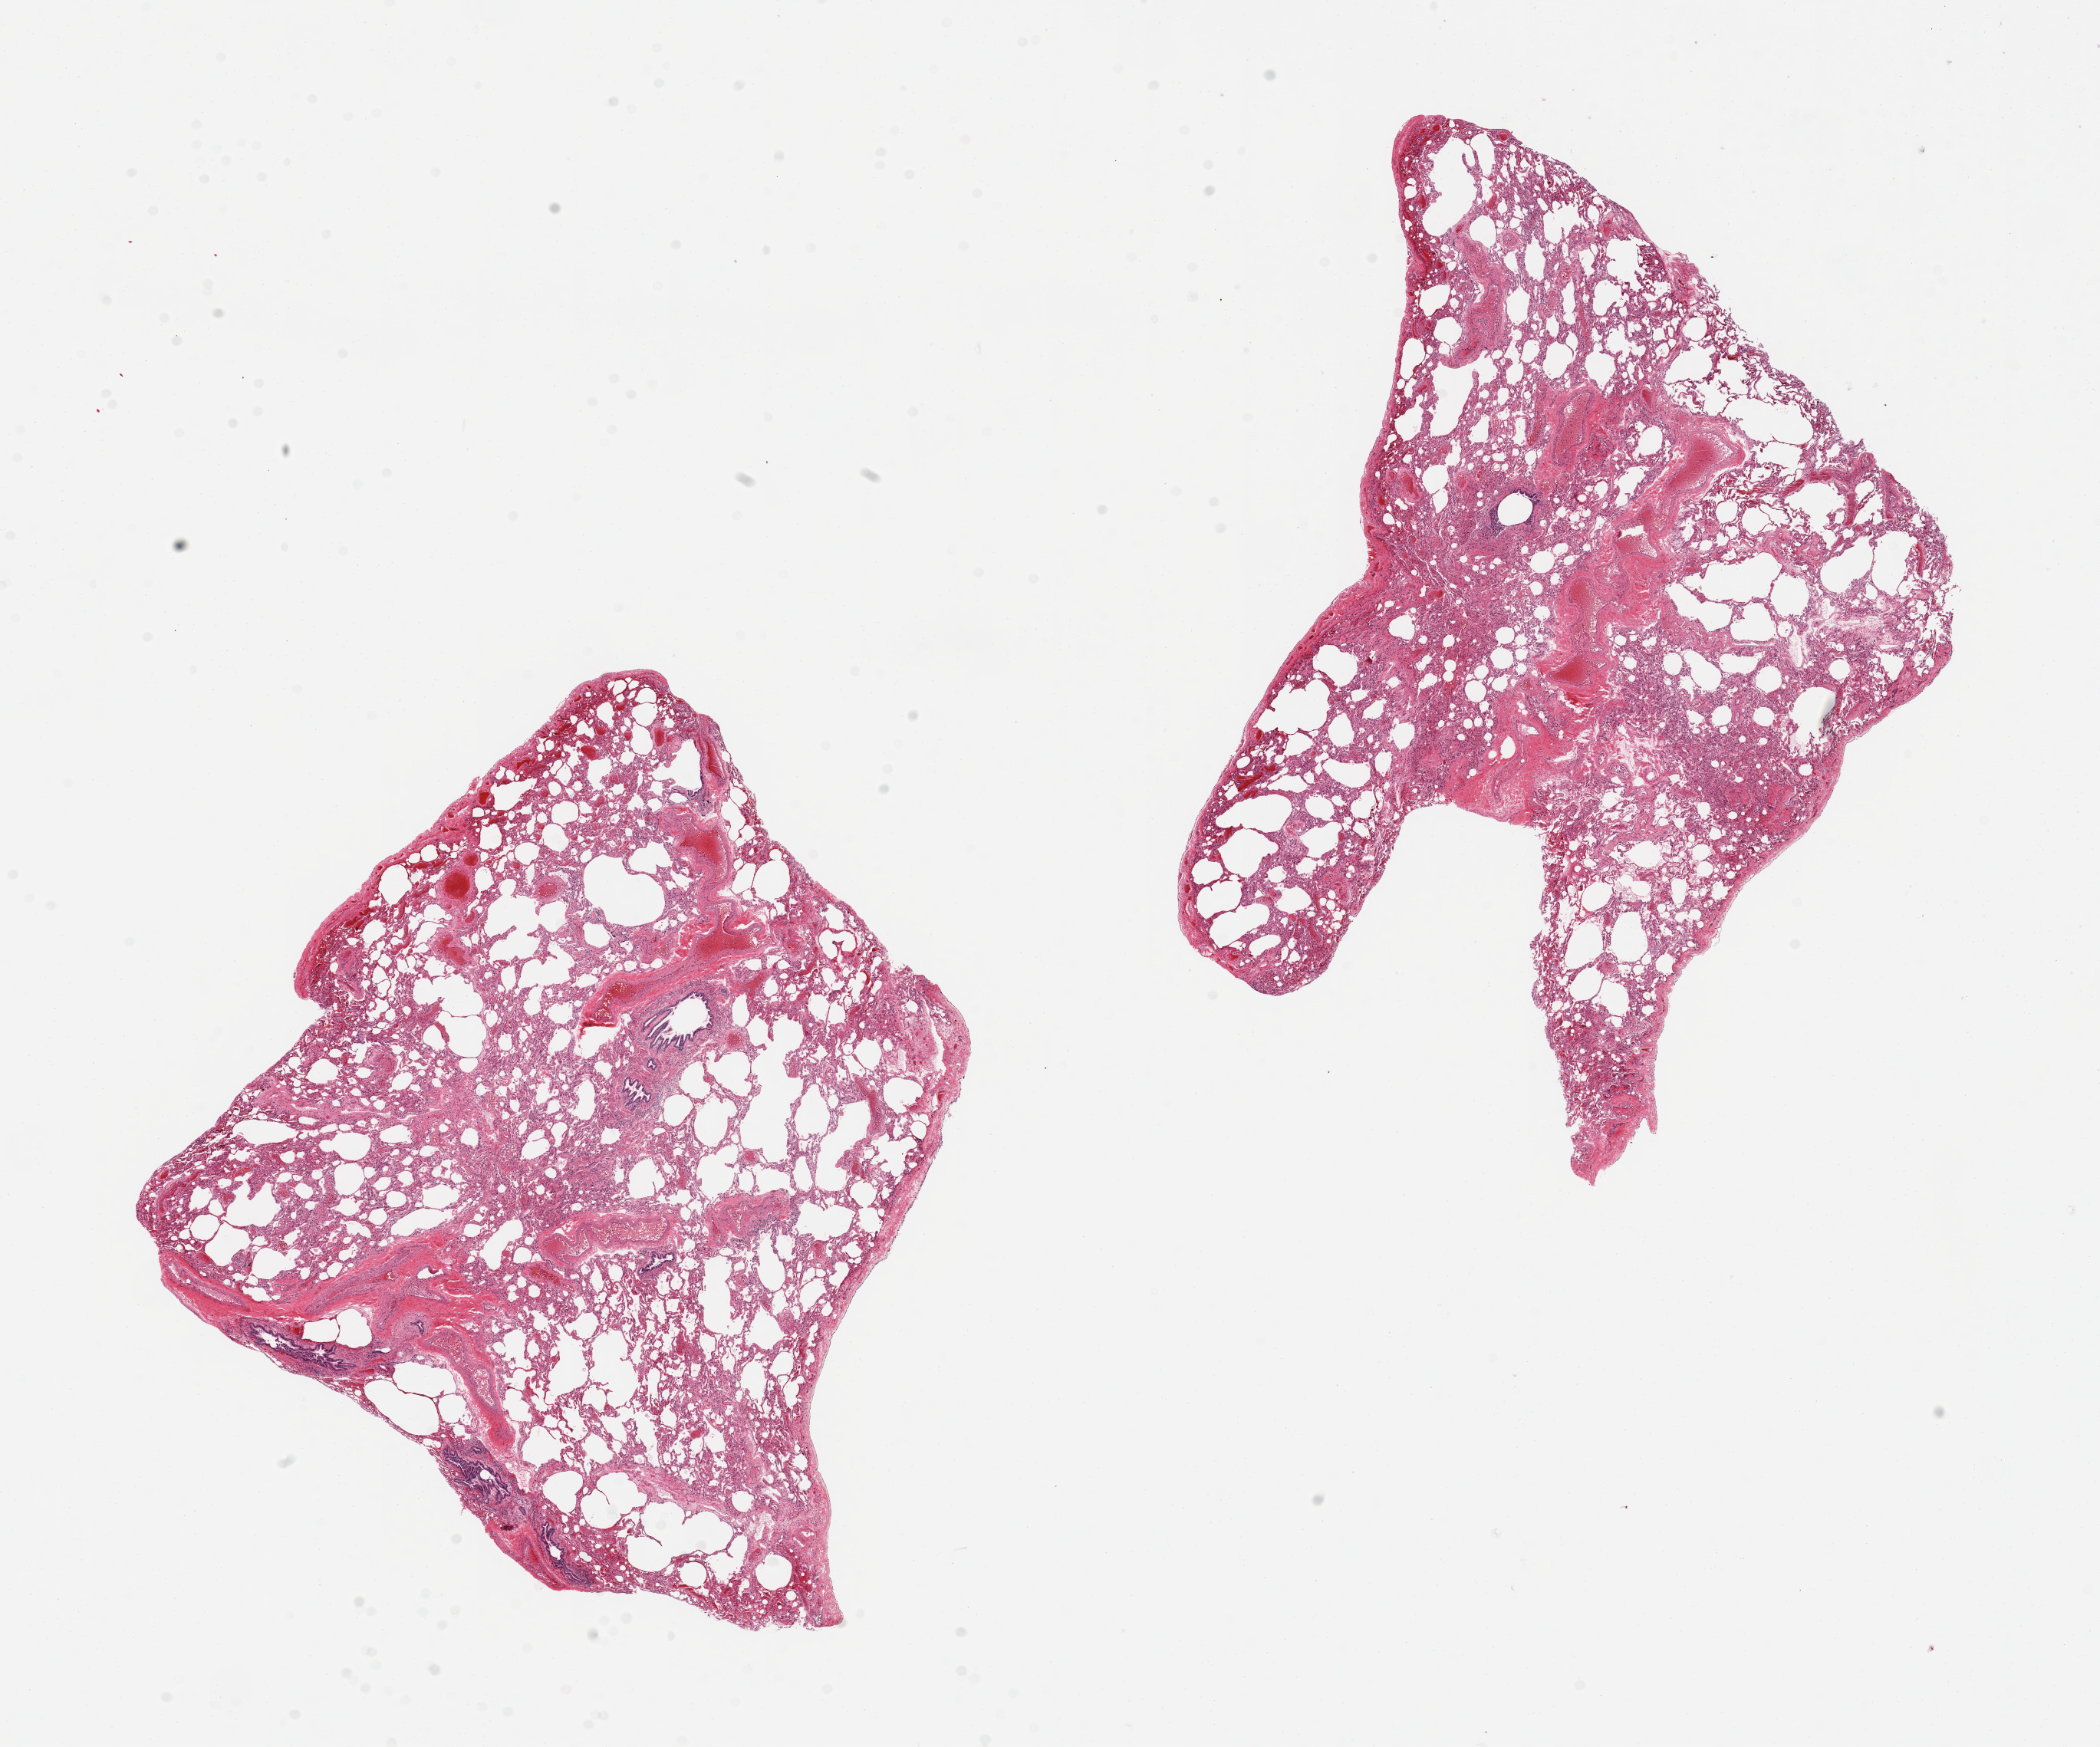
Digitized H&E-stained section, low-resolution overview of the scanned area, about 21.7 x 18.0 mm (from a 20x scan); PAXgene-fixed, paraffin-embedded tissue; sampled site (target tissue): lung; donor tissue sample.
Reviewer comment on this tissue sample: 2 pieces; emphysema.